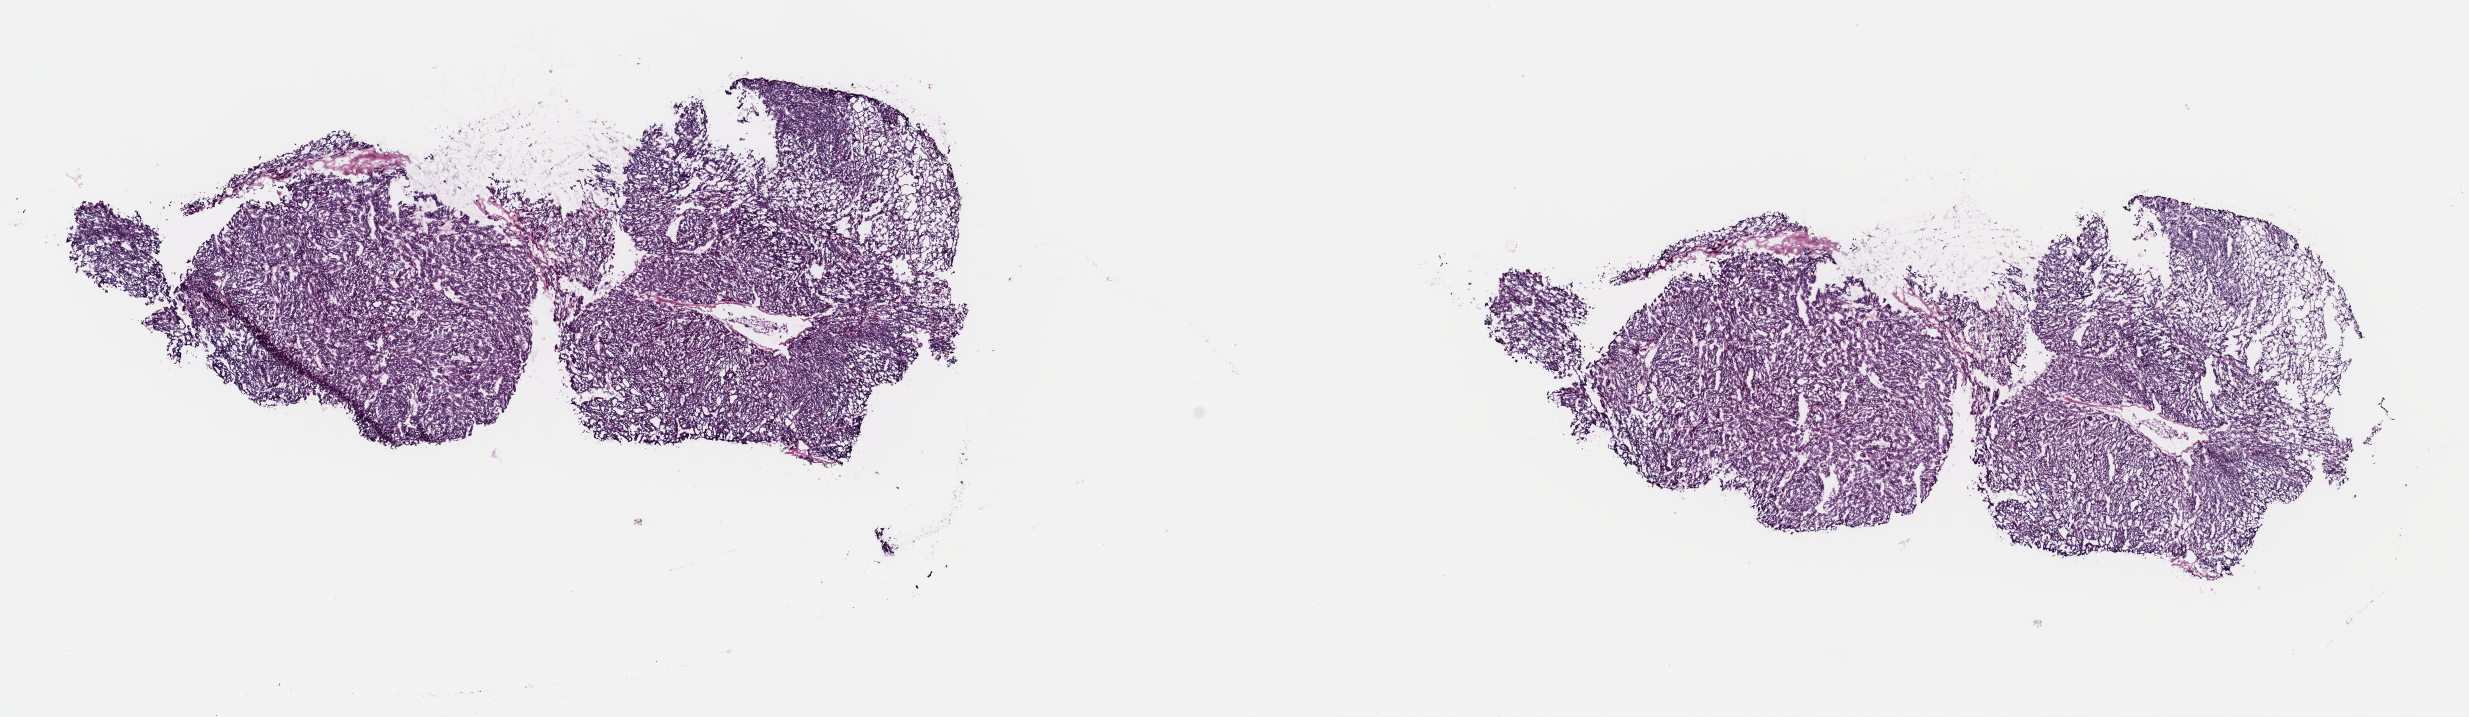
Digitized Hematoxylin and eosin (H&E) stained tissue section (whole slide), shown as a low-resolution overview of the whole scanned area (about 19.5 x 5.7 mm, slide scanned at 40x), frozen section from the top of the tissue portion, sample: primary tumour, thyroid. Patient: female, age at initial diagnosis 62 years. Pathologist review of this section (percent, as recorded): tumour cells 90%, tumour nuclei 90%, normal cells 0%, stromal cells 10%, necrosis 0%. Inflammatory infiltration, as recorded: lymphocyte infiltration 0%, monocyte infiltration 0%, neutrophil infiltration 0%.
TNM: T3 N0 MX. Histologic diagnosis: Carcinoma, NOS (thyroid gland). AJCC pathologic stage: III (7th edition).